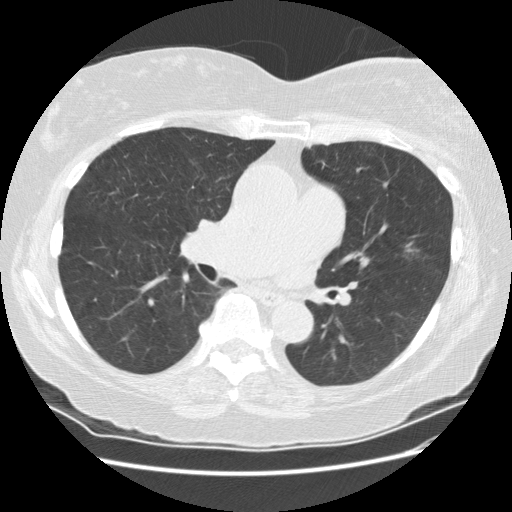
Axial slice from a low-dose chest CT screening exam. Second annual screen. Lung window (W 1500 / L -600 HU). Standard (soft-tissue) reconstruction kernel (STANDARD). 120 kVp. Slice 100 of 180 in the series. Female, age 71 years at enrolment. Former smoker at enrolment.
Expert-annotated lung lesion, bounding box <383,226,437,274> (left, top, right, bottom; pixels). Reader record for this screening exam (exam-level; its link to the box is not recorded): non-calcified nodule or mass ≥4 mm, lingula, 13 × 13 mm, poorly defined margins, ground glass attenuation, pre-existing on the prior screen: yes; interval growth: yes. Official screen result: positive, change unspecified: nodule(s) >= 4 mm or enlarging nodule(s), mass(es), or other non-specific abnormalities suspicious for lung cancer. Participant outcome: lung cancer diagnosed 26 days after this screen — adenocarcinoma, NOS, left upper lobe, well differentiated (G1), stage IA (AJCC 6th edition), 11 mm at pathology.